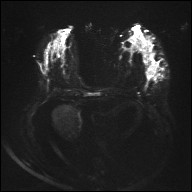
Breast MRI, one axial slice. Slice 15 of 32 in the series (ordered by position). Diffusion-weighted series; image 2 of 4 stored at this slice position (different b-values; order by instance number). 1.5 T. 4 mm slice thickness. 192 × 192 image matrix. Female patient.
Outlined on this slice (expert manual segmentation):
- tumour on diffusion-weighted imaging: bounding box [x1, y1, x2, y2] px = [147, 66, 155, 75]